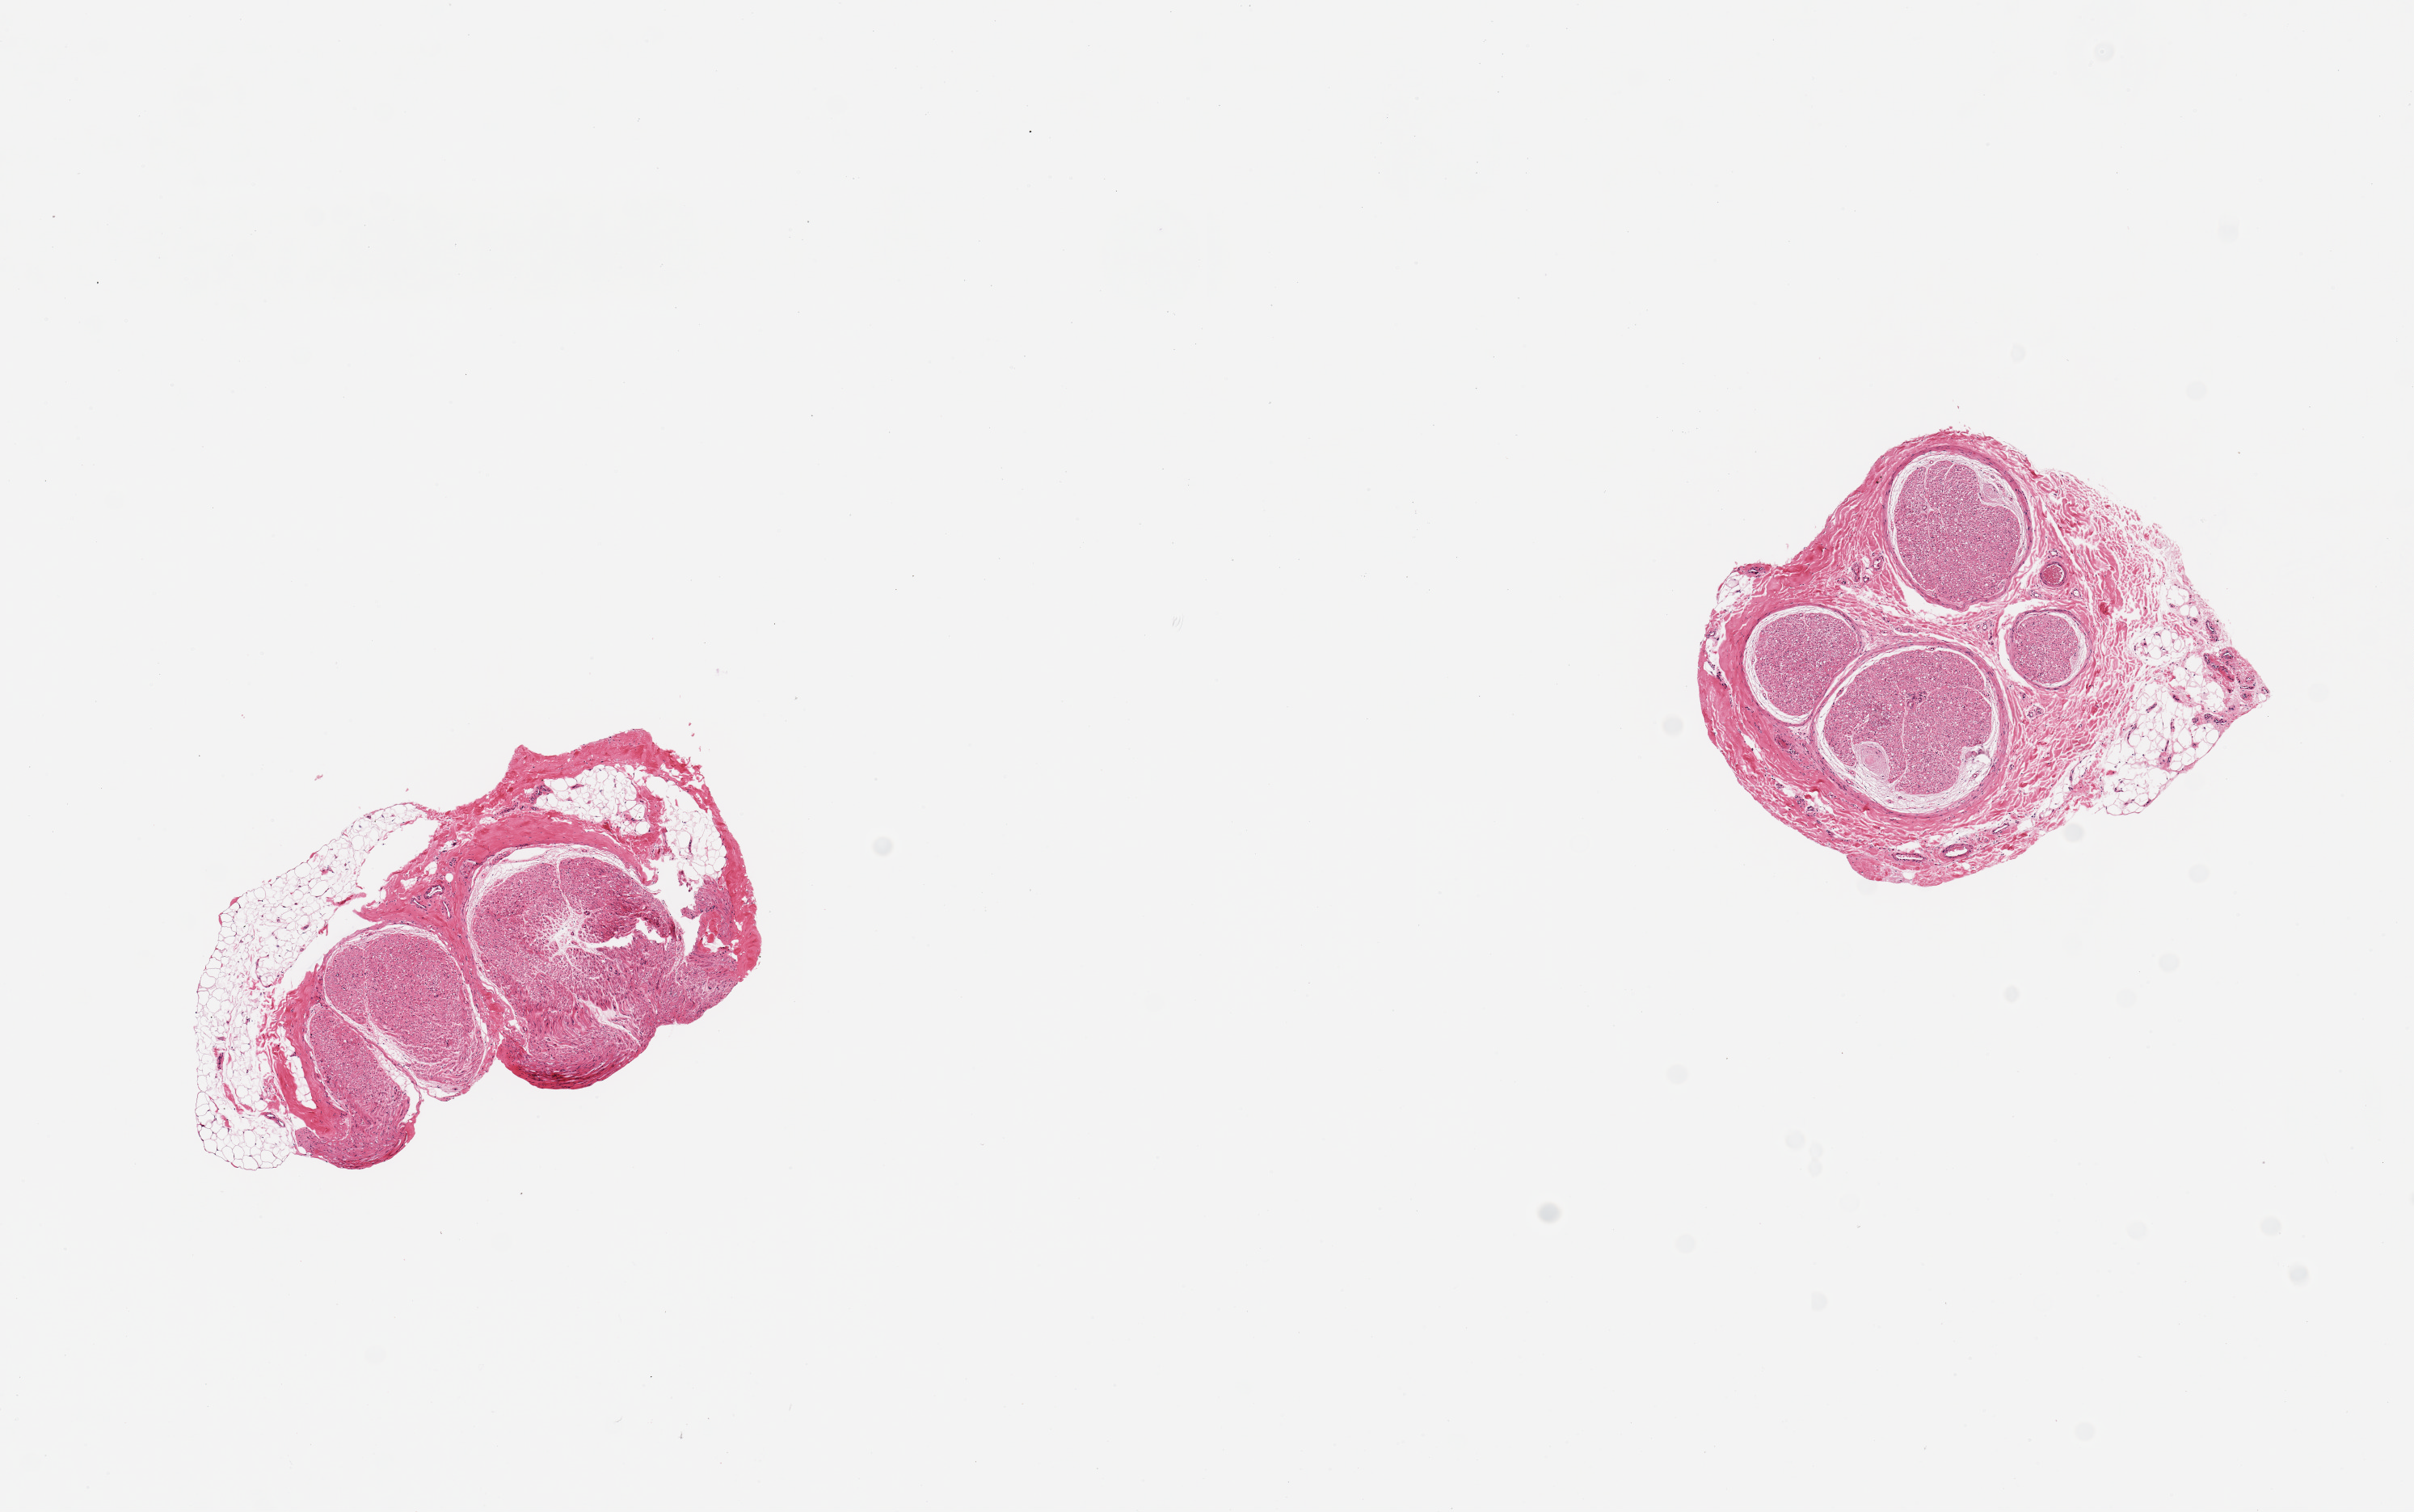
Whole-slide image, H&E stain, whole scanned area (about 11.8 x 7.4 mm, acquisition: 20x scan) shown as a low-resolution overview, PAXgene-fixed, paraffin-embedded tissue, sampled site (target tissue): tibial nerve, tissue donor sample. Male donor.
Pathologist's review note for this sample: 2 pieces ~3x1.5, & 2x2 mm; embedded in ~30% stroma & fat.